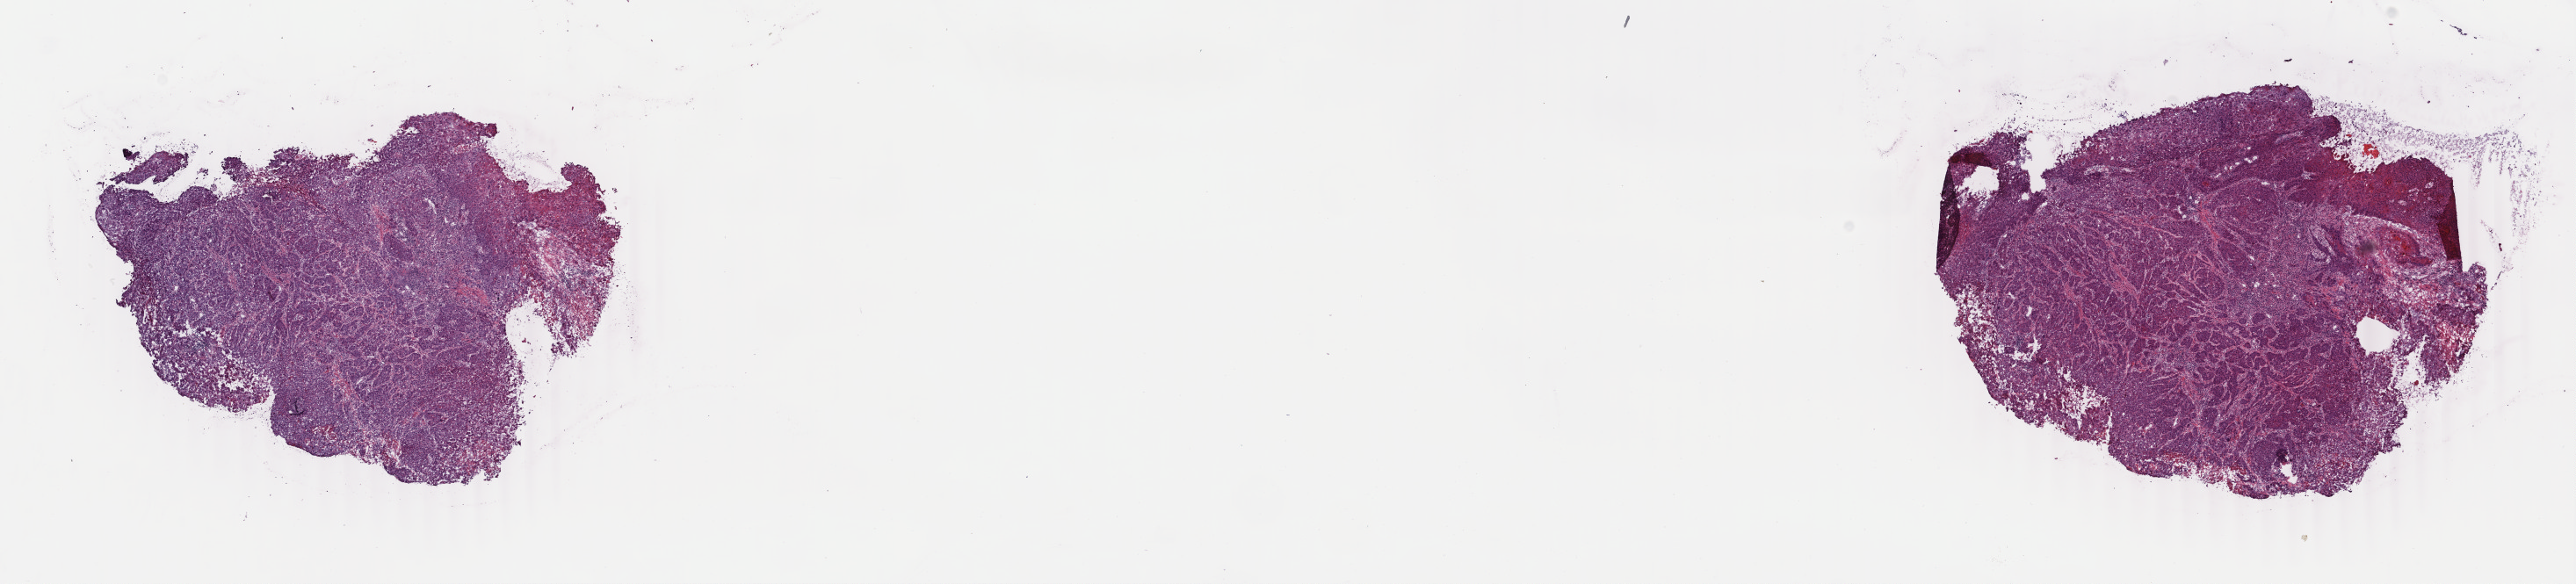
Digitized H&E-stained tissue section (whole slide), shown as a low-resolution overview of the whole scanned area (about 23.3 x 5.3 mm, acquisition: 40x scan). Frozen section from the top of the tissue portion. Head and neck, primary tumour sample. Male, age 61 years at initial diagnosis. Histologic grade: G2 (moderately differentiated). Pathologist review of this section (percent, as recorded): tumour cells 85%, tumour nuclei 90%, normal cells 0%, stromal cells 14%, necrosis 1%. Infiltration values recorded for this section: lymphocyte infiltration 12%, monocyte infiltration 4%, neutrophil infiltration 2%.
Diagnosis: Squamous cell carcinoma, keratinizing, NOS (tongue, NOS). AJCC pathologic stage: III (7th edition). Lymph nodes positive (case pathology): 0 of 15 examined.